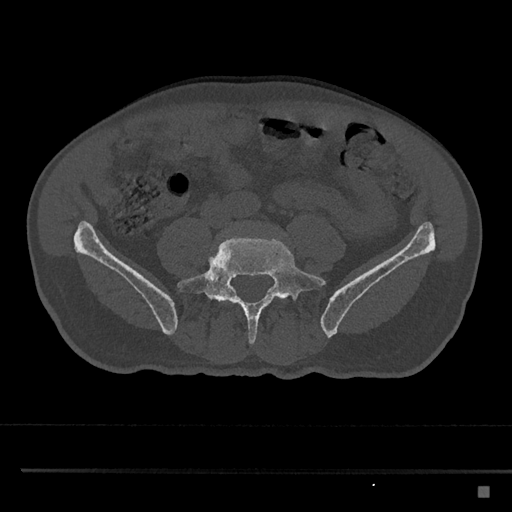
CT including the spine, one axial slice. Position 590 of 797 along the scan axis. 120 kVp. Bone window (W 1800 / L 400 HU). 0.5 mm slice thickness. 512 × 512 image matrix, field of view 391 × 391 mm. Male patient, age 59 years. Case-level facts recorded for this patient, not image findings: primary cancer: prostate.
Outlined on this slice (semi-automatic segmentation, software-assisted and operator-edited):
- L5 vertebra: box from (x=177, y=235) to (x=326, y=345) px